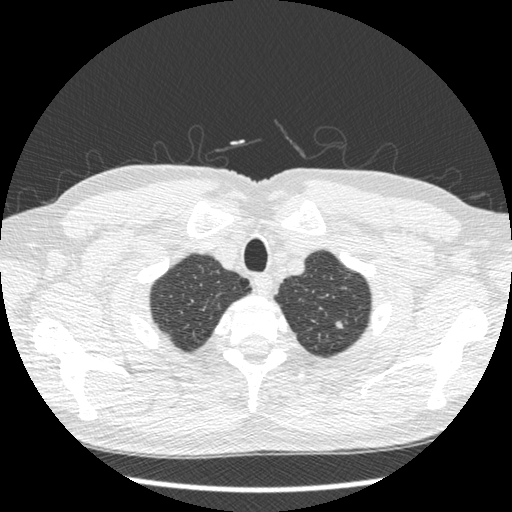
Low-dose screening chest CT, one axial slice; position 406 of 439 along the scan axis; reconstruction kernel STANDARD; 120 kVp; lung window (W 1500 / L -600 HU); 512 × 512 image matrix, field of view 340 × 340 mm.
Annotated regions visible in this slice (manually delineated by an expert):
- lesion 1 (nodule, upper lobe of left lung): bounding box [x1, y1, x2, y2] px = [335, 321, 344, 329]